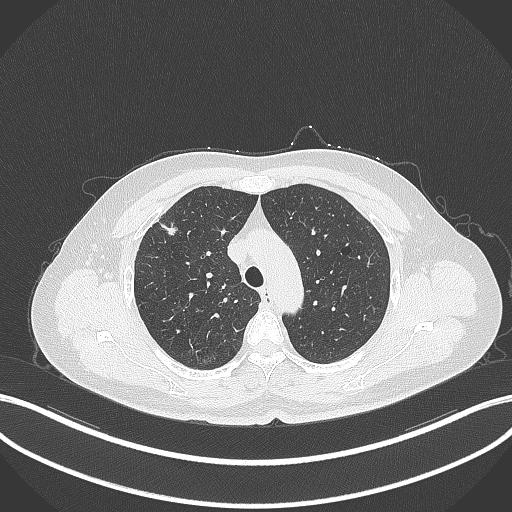
Chest CT, one axial slice. Slice 273 of 353 in the series (ordered by position). Reconstruction kernel B70f. 120 kVp. Lung window (W 1500 / L -600 HU). 1 mm slice thickness. 512 × 512 image matrix, field of view 400 × 400 mm. Female patient, age 56 years. Case-level facts recorded for this patient, not image findings: clinical TNM (as recorded): T1c N0 M0.
Annotated regions visible in this slice (bounding box drawn by a radiologist):
- lung tumour (recorded histology: adenocarcinoma): bounding box <161,220,182,239> (left, top, right, bottom; pixels)